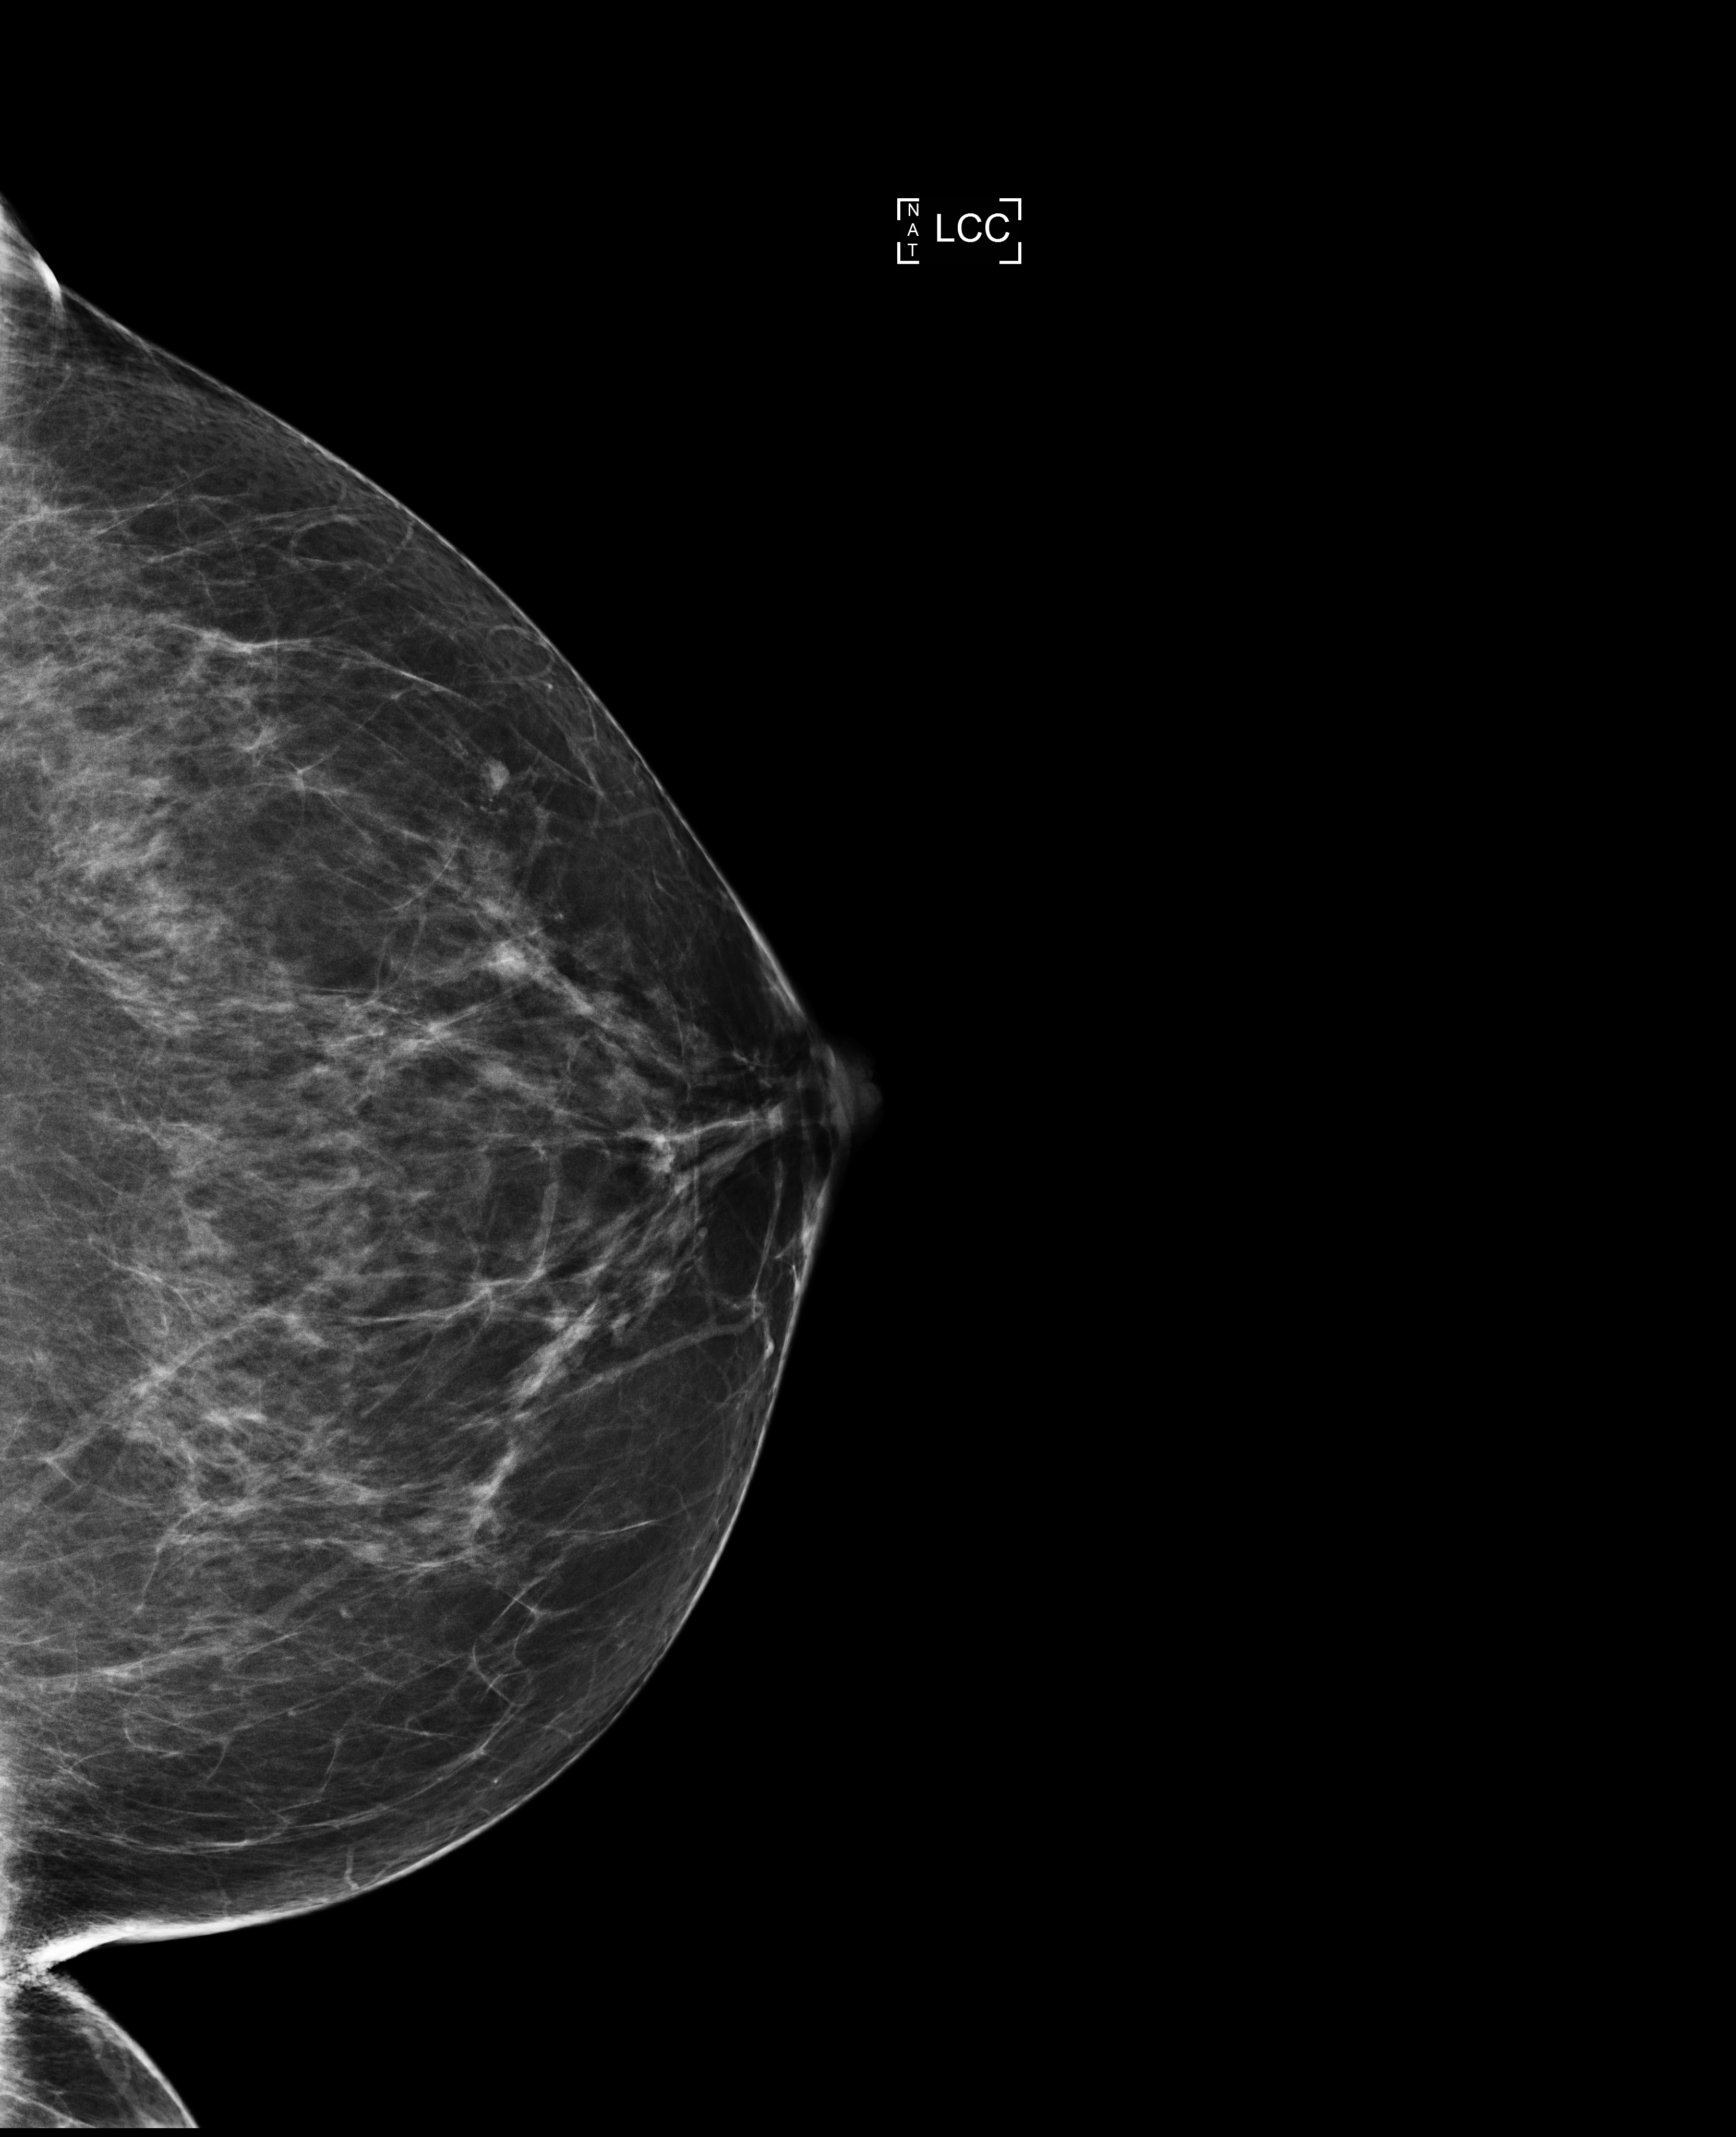
Digital mammogram (FFDM), left breast, craniocaudal (CC) view, screening examination, compressed breast thickness 90 mm. Female patient, age 52 years.
BI-RADS breast density category at the screening exam (both breasts, scale 1–4): 2. Final BI-RADS category for the screening round (tomosynthesis exam, both breasts): category 1. Recall: no recall after this screen.